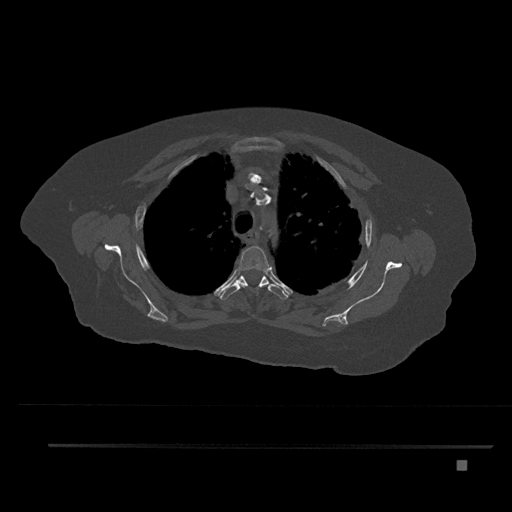
CT including the spine, one axial slice; position 619 of 797 along the scan axis; reconstruction kernel Br40s/3; 120 kVp; bone window (W 1800 / L 400 HU); 0.5 mm slice thickness; 512 × 512 image matrix. Patient: female, 76 years. From the clinical record (not read from this slice): primary cancer: lung.
Outlined on this slice (semi-automatically segmented with operator editing):
- T3 vertebra: bounding box (x1, y1, x2, y2) in pixels: (231, 246, 271, 287)
- T4 vertebra: (219, 276, 289, 300)